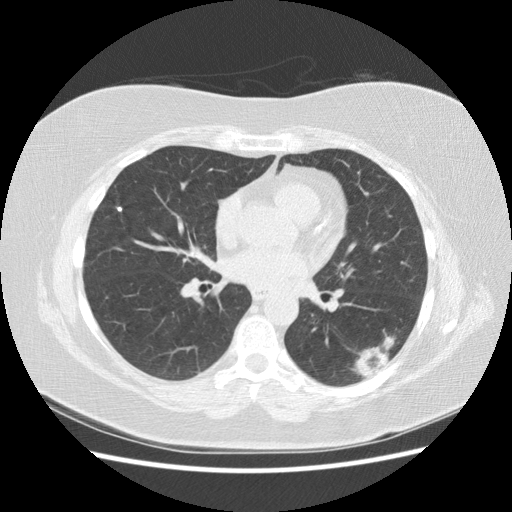
Axial slice from a low-dose chest CT screening exam; third annual screen; lung window (W 1500 / L -600 HU); 2.5 mm slice thickness; standard (soft-tissue) reconstruction kernel (STANDARD). Female participant, aged 57 years at enrolment. Current smoker at enrolment.
Lesion marked by an expert reader, bounding box (x1, y1, x2, y2) in pixels: (336, 324, 407, 388). Reader record for this screening exam (exam-level; its link to the box is not recorded): non-calcified nodule or mass ≥4 mm, left lower lobe, 40 × 20 mm, poorly defined margins, mixed attenuation, pre-existing on the prior screen: yes; interval growth: yes. Lung cancer was diagnosed 55 days after this screen: squamous cell carcinoma, NOS, left lower lobe, poorly differentiated (G3), stage IB (AJCC 6th edition), 40 mm at pathology.